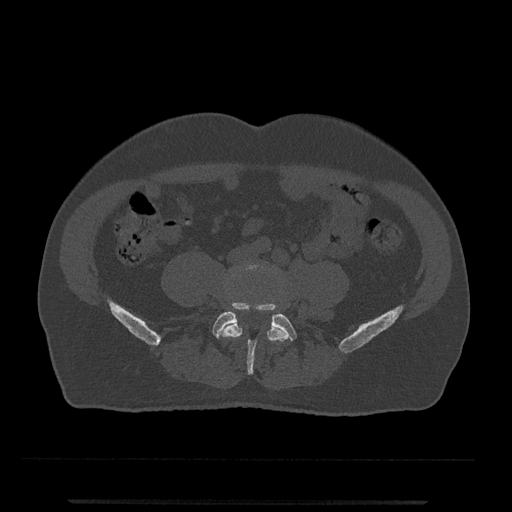
CT including the spine, one axial slice. Position 98 of 797 along the scan axis. Bone window (W 1800 / L 400 HU). 0.5 mm slice thickness. 512 × 512 image matrix. Patient: male, 63 years. Case-level facts recorded for this patient, not image findings: primary cancer: prostate.
Annotated regions visible in this slice (semi-automatically segmented with operator editing):
- L4 vertebra: bounding box [x1, y1, x2, y2] px = [220, 263, 289, 371]
- L5 vertebra: [212, 302, 297, 375]